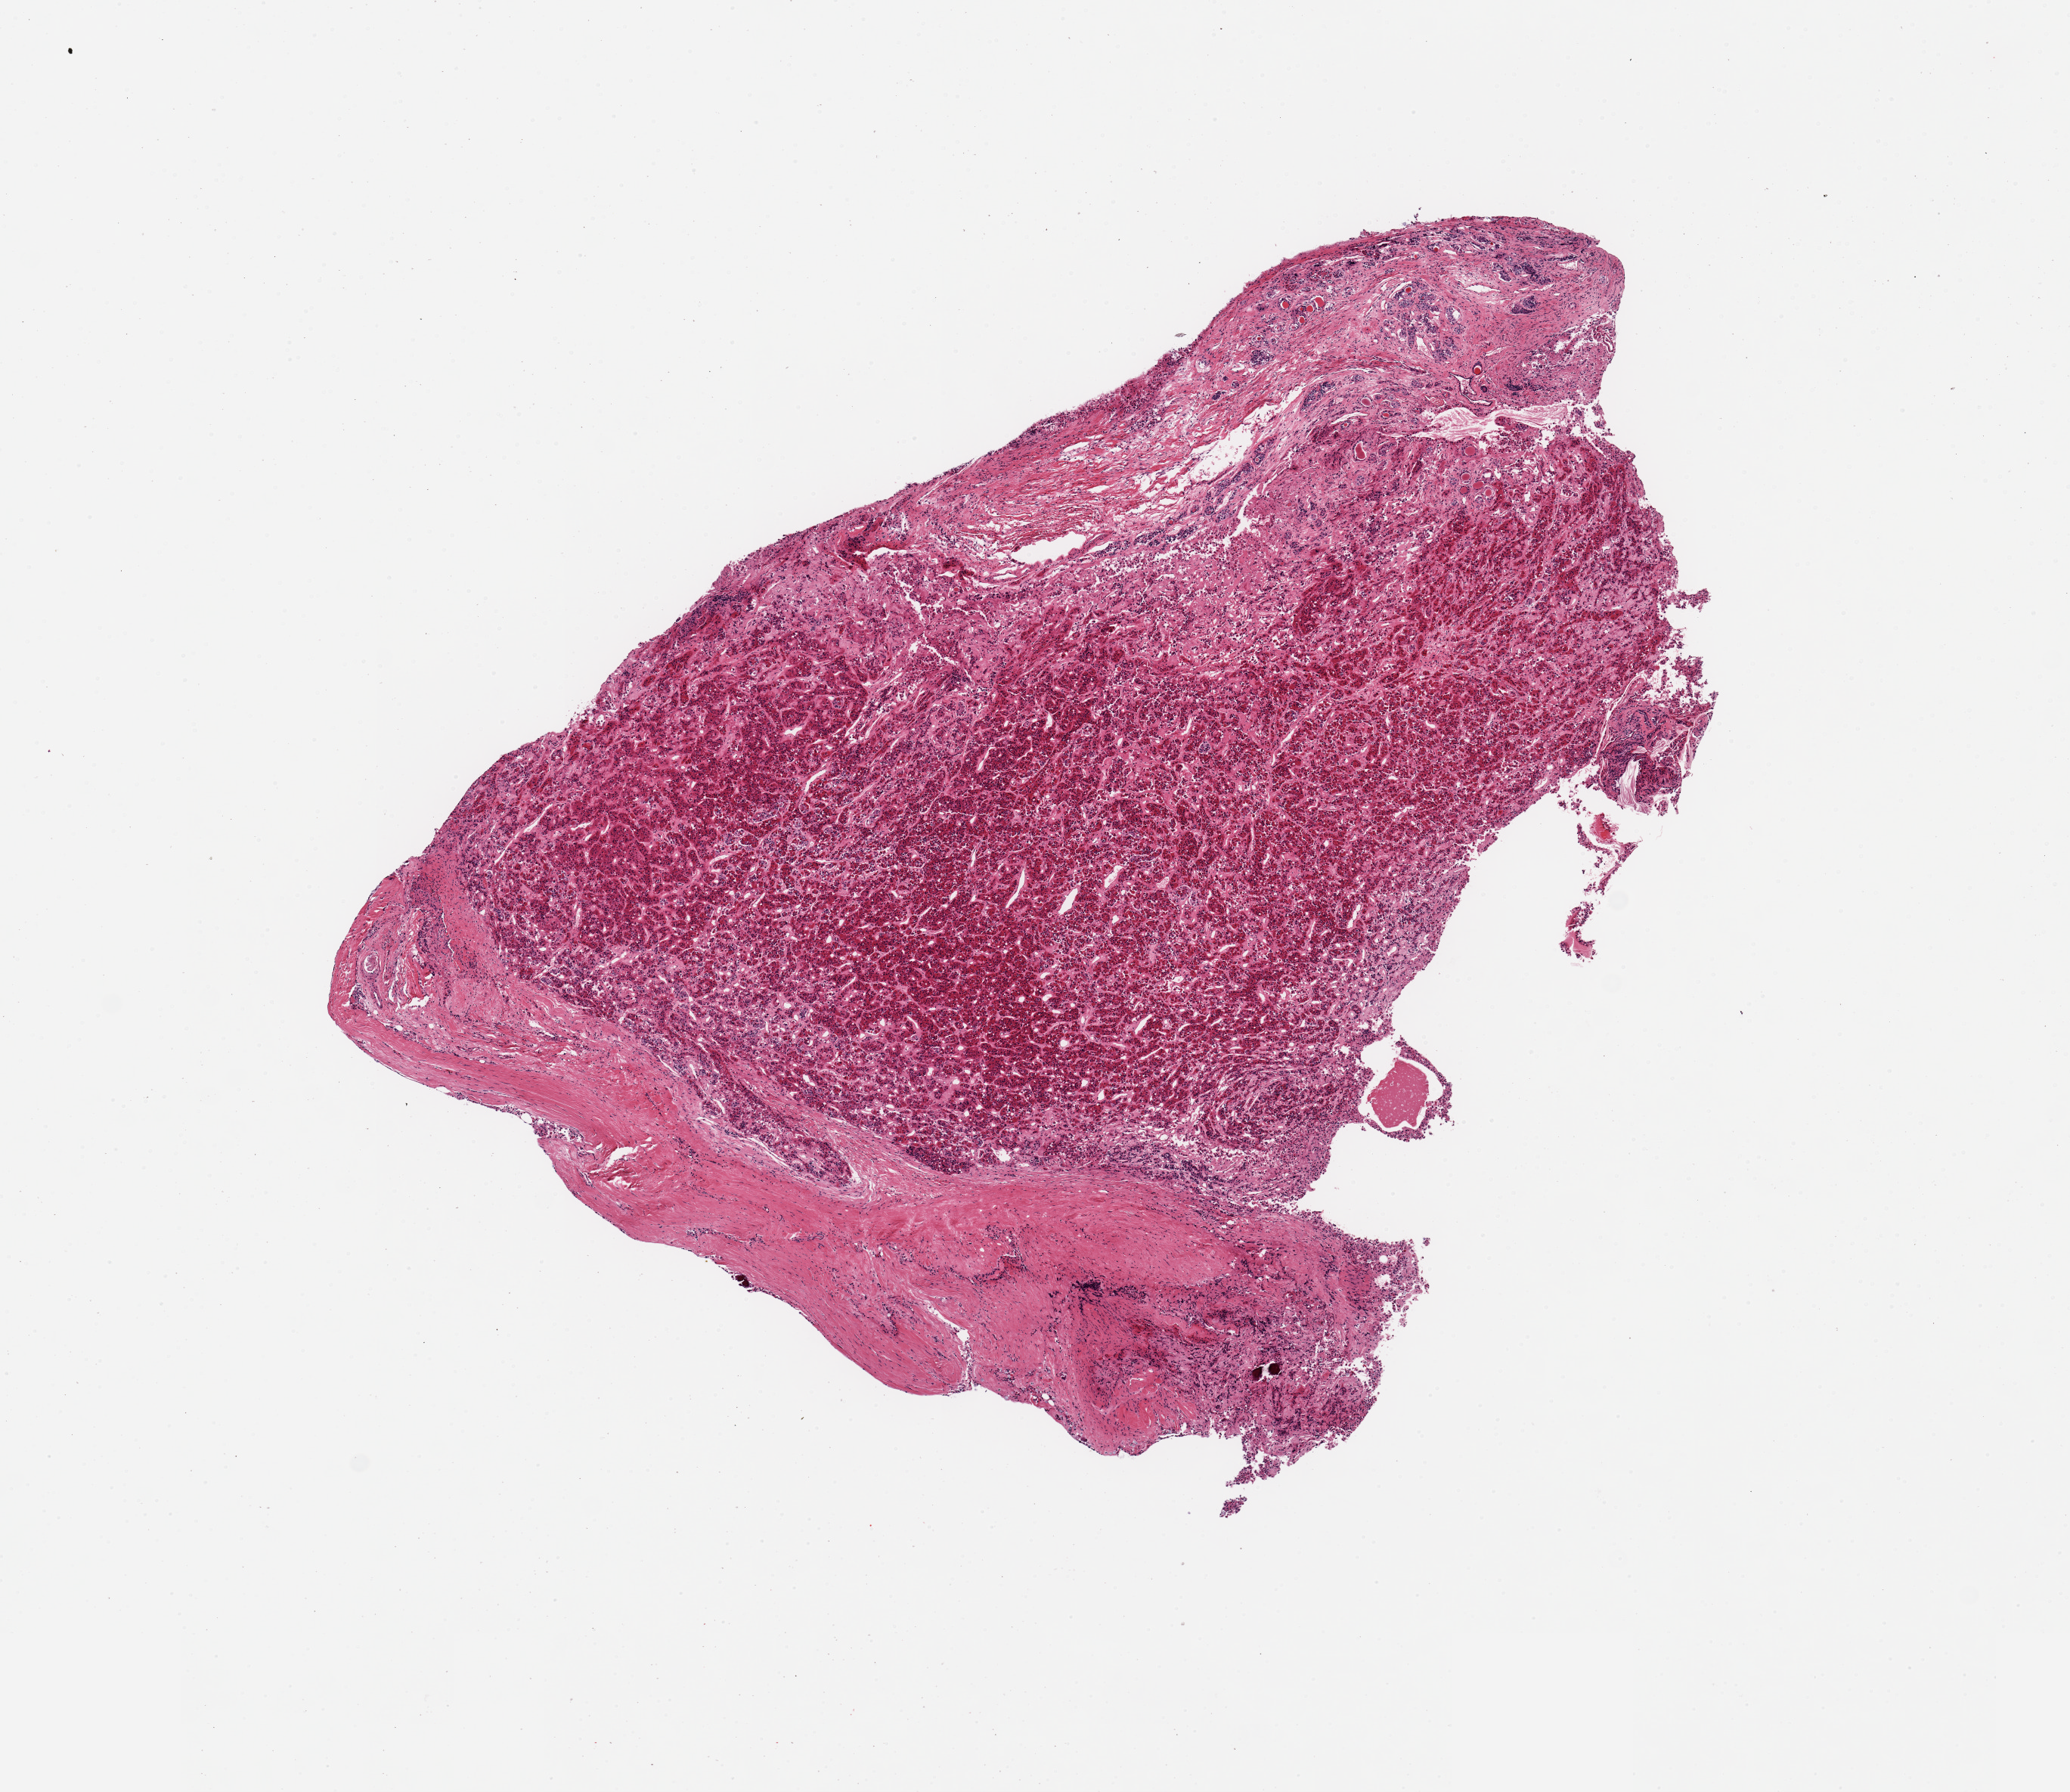
Hematoxylin and eosin (H&E) whole-slide image, brightfield — shown as a low-resolution overview of the whole scanned area (about 10.8 x 9.4 mm). PAXgene-fixed paraffin-embedded (PFPE) section. Section of pituitary (target tissue). Donor tissue sample.
Pathologist's review note for this sample: 1 piece; mild to moderate autolysis of adenohypophysis; attached rim of dense fibrovasular tissue with small calcifications likely dura.